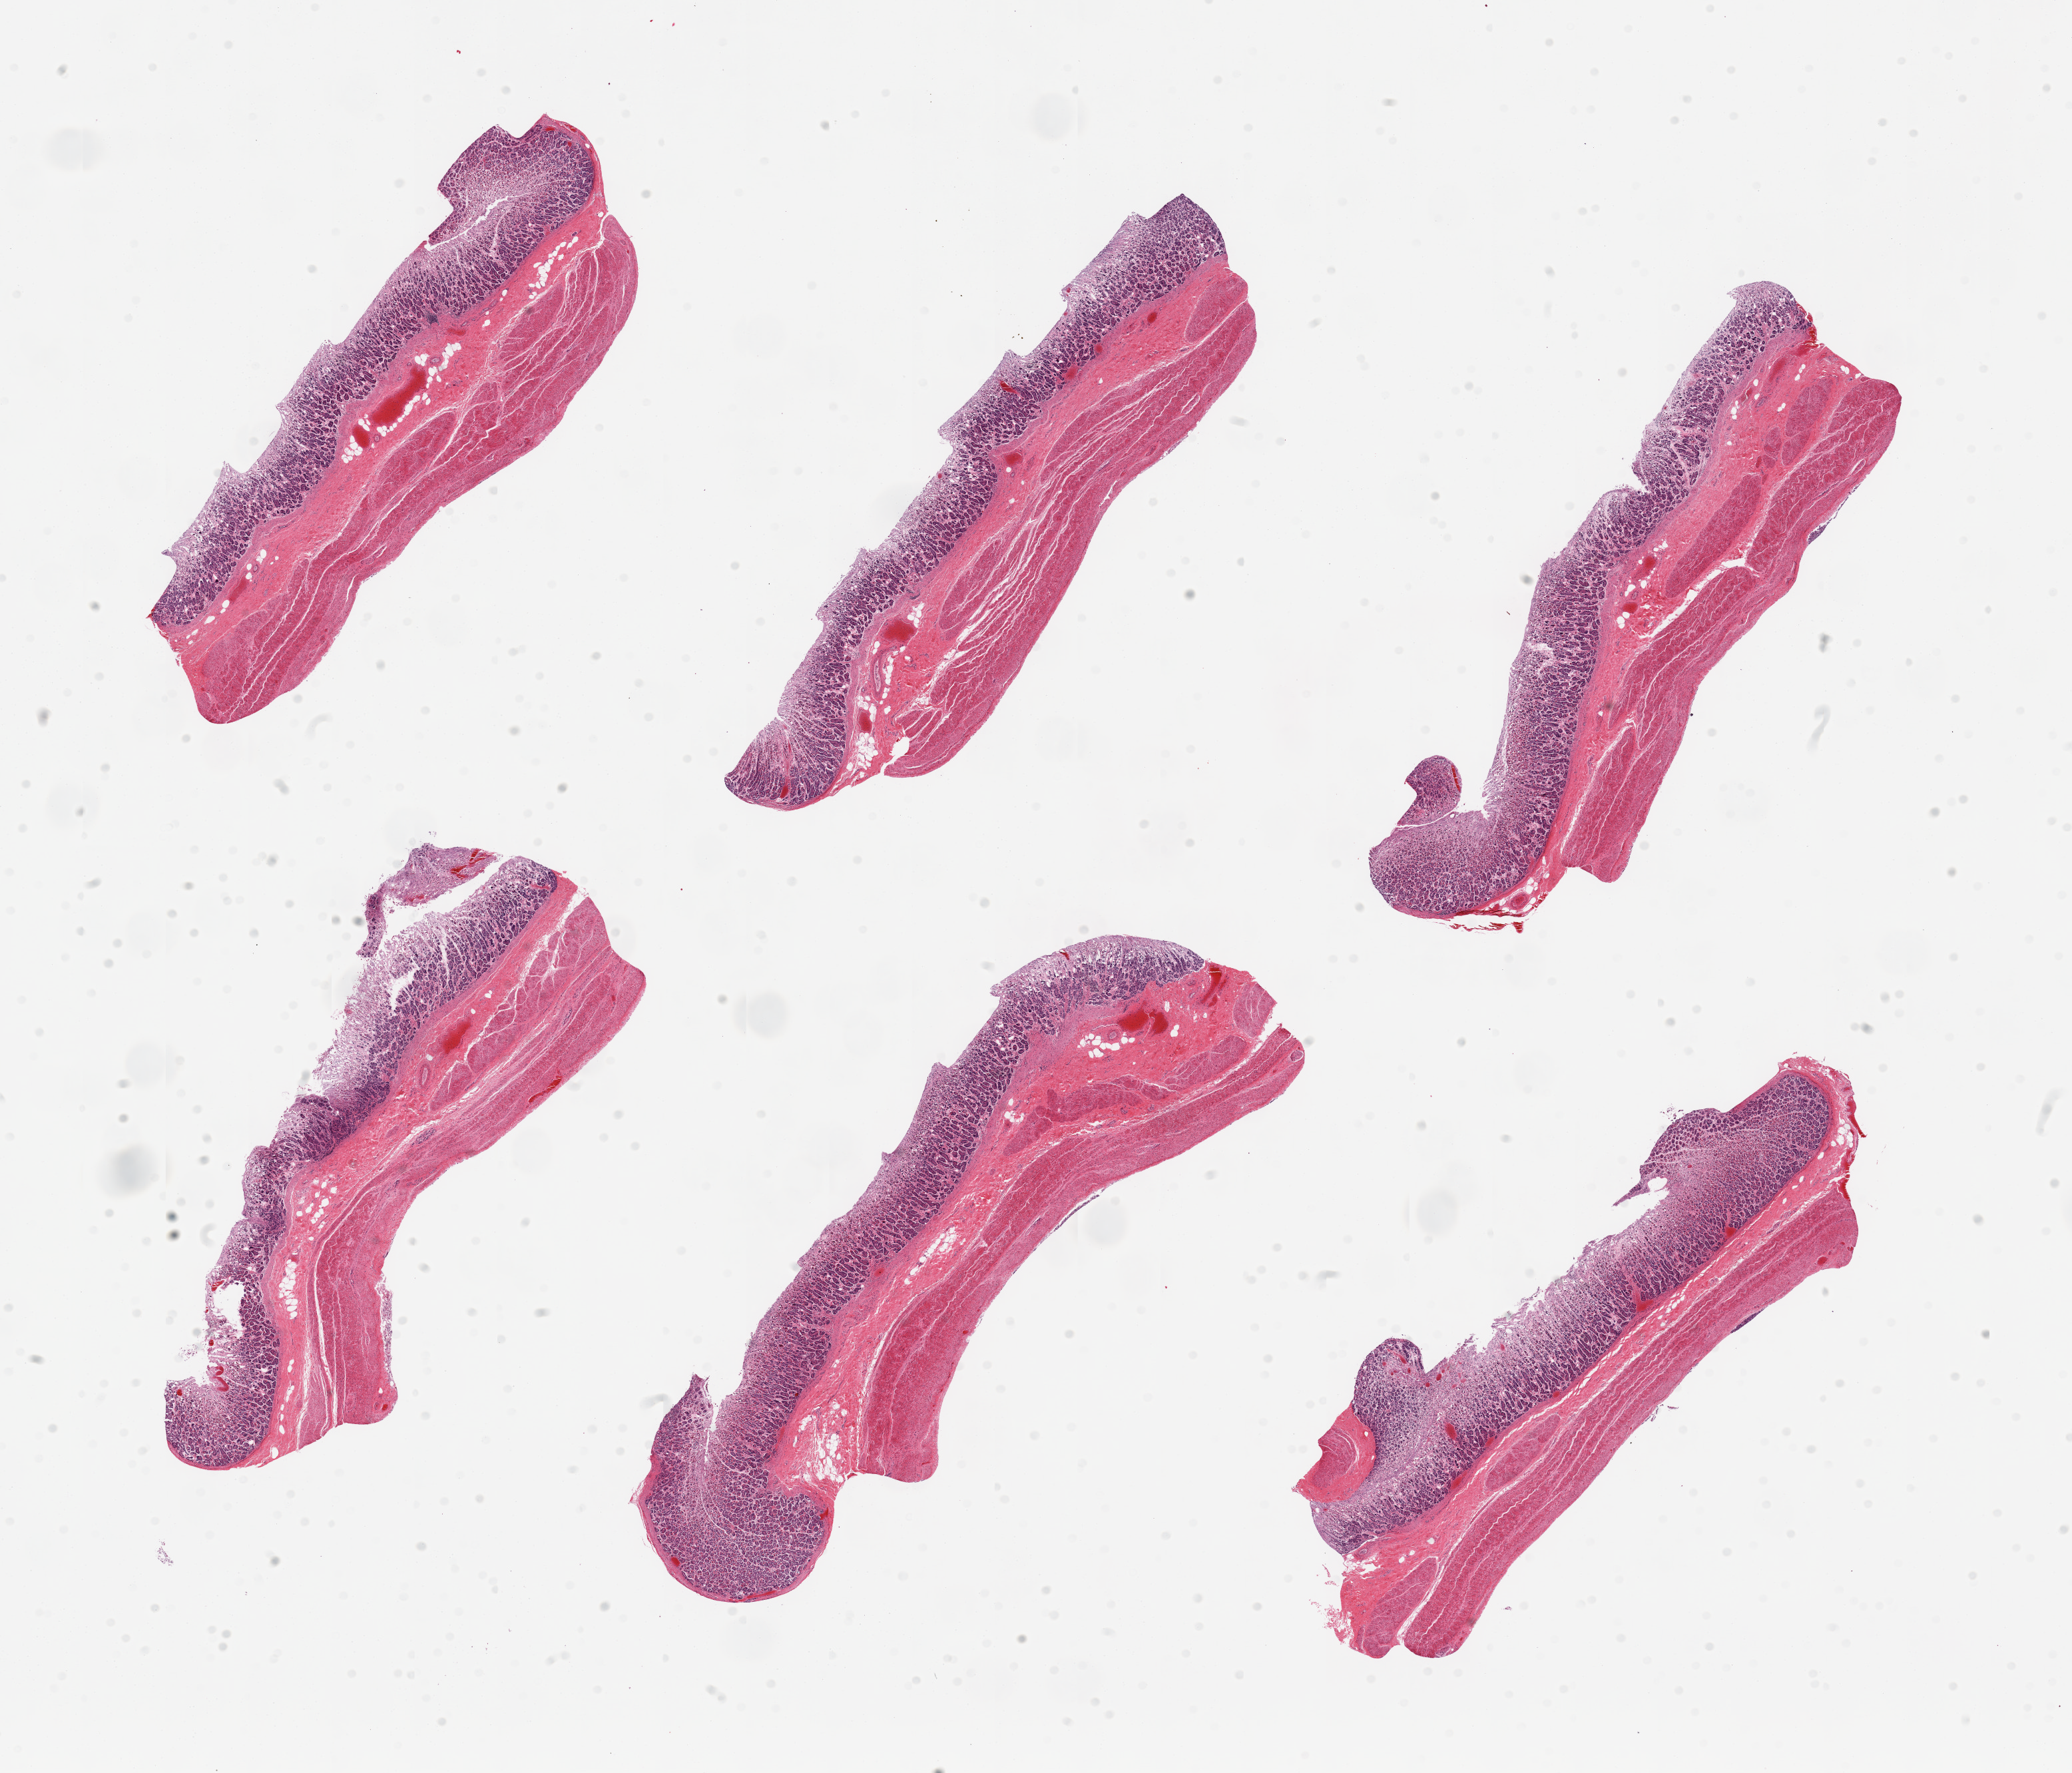
Digitized haematoxylin and eosin-stained section — a low-resolution overview of the entire scanned area, about 24.6 x 21.1 mm (from a 20x scan); PAXgene-fixed, paraffin-embedded tissue; sampled site (target tissue): stomach; donor tissue sample. Donor: male.
* review note (as recorded): 6 pieces, moderately autolyzed mucosa and muscularis